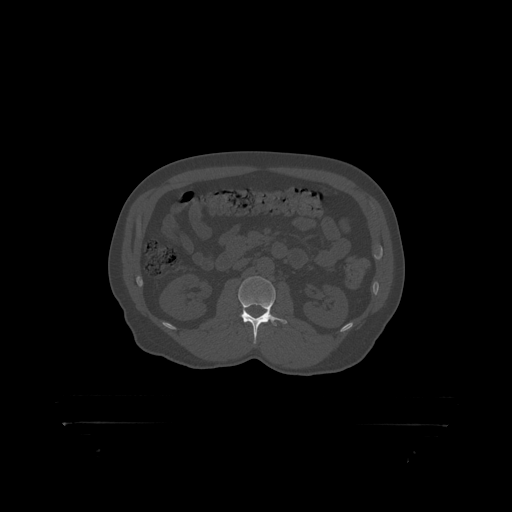
CT including the spine, one axial slice; slice 294 of 399 in the series (ordered by position); reconstruction kernel STANDARD; bone window (W 1800 / L 400 HU); 512 × 512 image matrix, field of view 650 × 650 mm. Male patient, age 46 years. From the clinical record (not read from this slice): primary cancer: skin.
Annotated regions visible in this slice (semi-automatic segmentation, software-assisted and operator-edited):
- L2 vertebra: bounding box (x1, y1, x2, y2) in pixels: (238, 276, 276, 319)